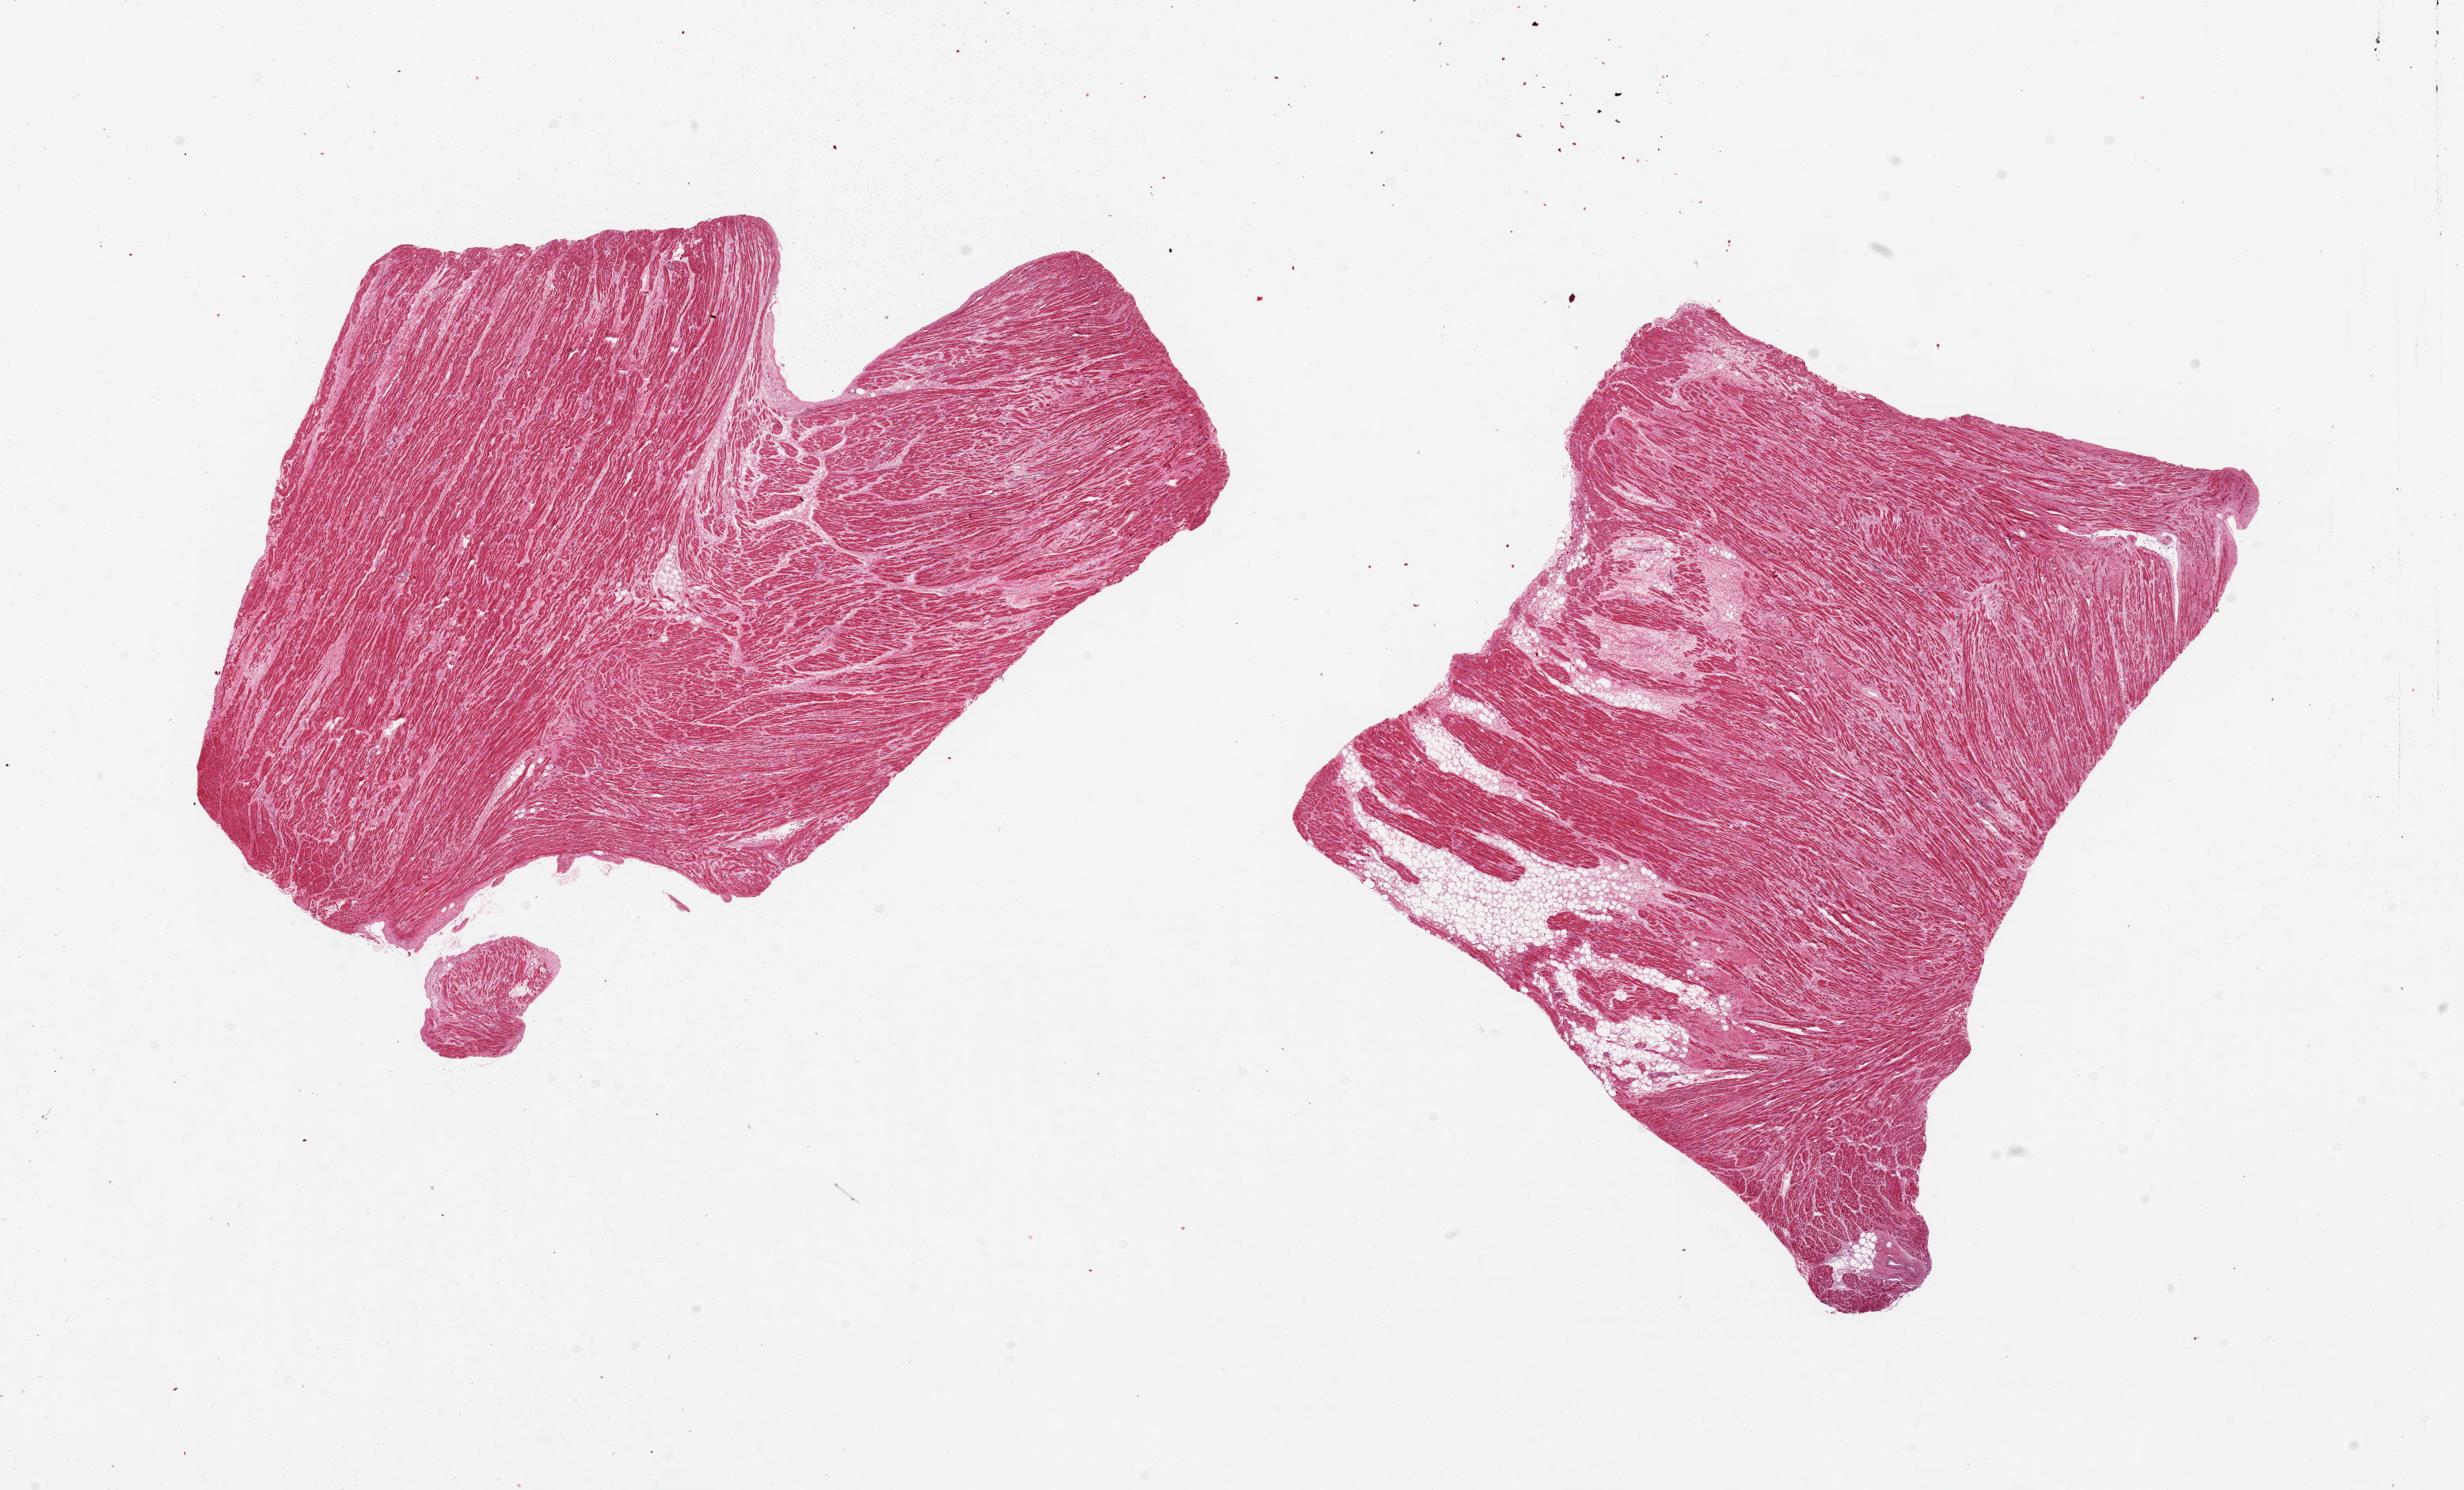
Hematoxylin and eosin (H&E) whole-slide image, brightfield, low-resolution overview of the scanned area, about 24.6 x 14.9 mm (acquisition: 20x scan). PAXgene-fixed, paraffin-embedded tissue. Target tissue: auricular appendage. Tissue donor sample.
Reviewer comment on this tissue sample: 2 pieces, noa abnormalities.